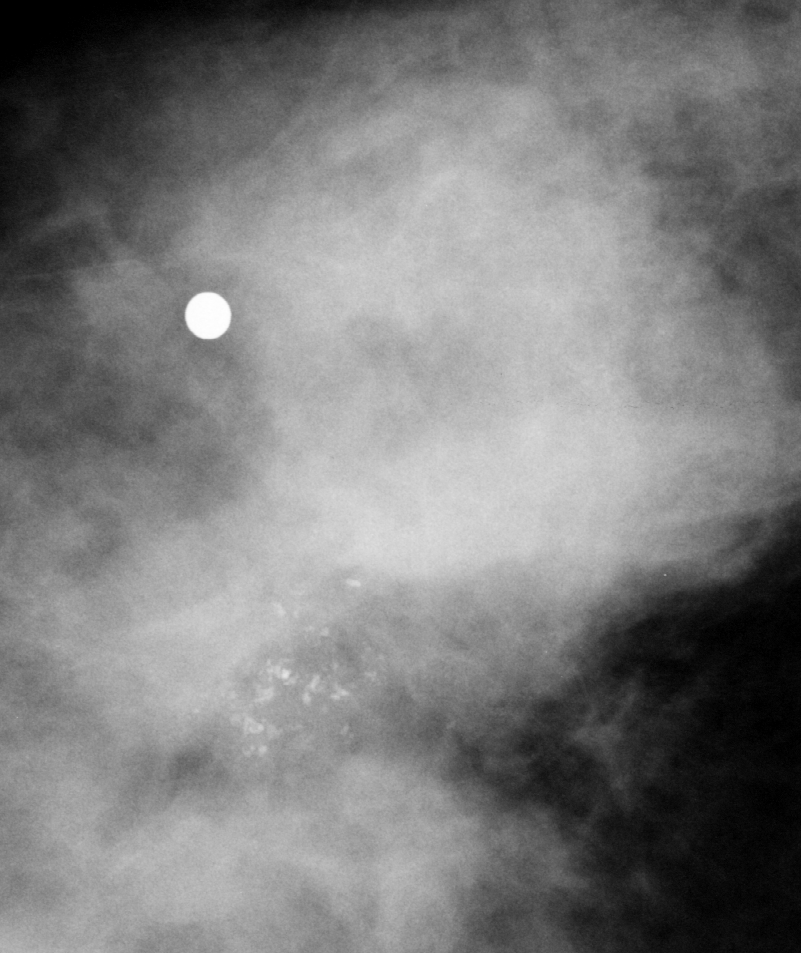
Crop from a digitized film mammogram around one marked abnormality, right breast, CC view, BI-RADS breast density category 3 (scale 1–4).
Finding: calcifications, morphology pleomorphic, distribution clustered; BI-RADS assessment category 5; pathology result (as recorded, not read from the image): malignant.